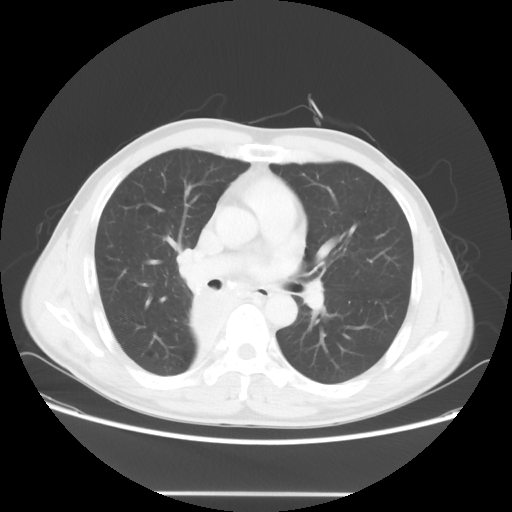
Chest CT, one axial slice. Slice 35 of 62 in the series (ordered by position). Reconstruction kernel STANDARD. 120 kVp. Lung window (W 1500 / L -600 HU). 512 × 512 image matrix. Patient: male, 47 years. From the clinical record (not read from this slice): clinical TNM (as recorded): T2 N0 M0.
Structures marked on this image (bounding box drawn by a radiologist):
- lung tumour (recorded histology: squamous cell carcinoma): bounding box <179,271,247,338> (left, top, right, bottom; pixels)